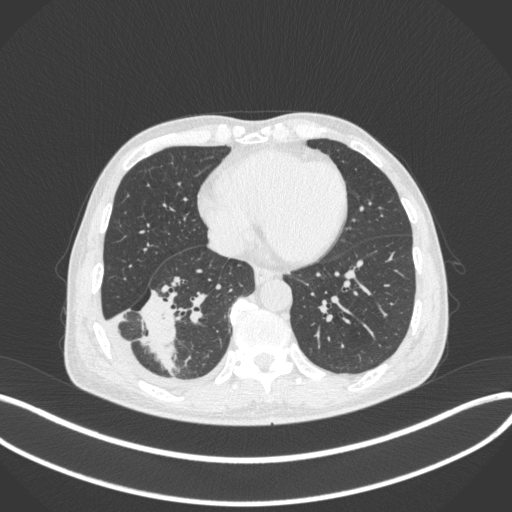
Chest CT, one axial slice; slice 132 of 385 in the series (ordered by position); reconstruction kernel B31f; lung window (W 1500 / L -600 HU); 1 mm slice thickness; 512 × 512 image matrix. Male patient, age 64 years. From the clinical record (not read from this slice): clinical TNM (as recorded): T3 N0 M0.
Annotated regions visible in this slice (rectangle marked by the reading radiologist):
- lung tumour (recorded histology: adenocarcinoma): bounding box (x1, y1, x2, y2) in pixels: (134, 282, 185, 377)